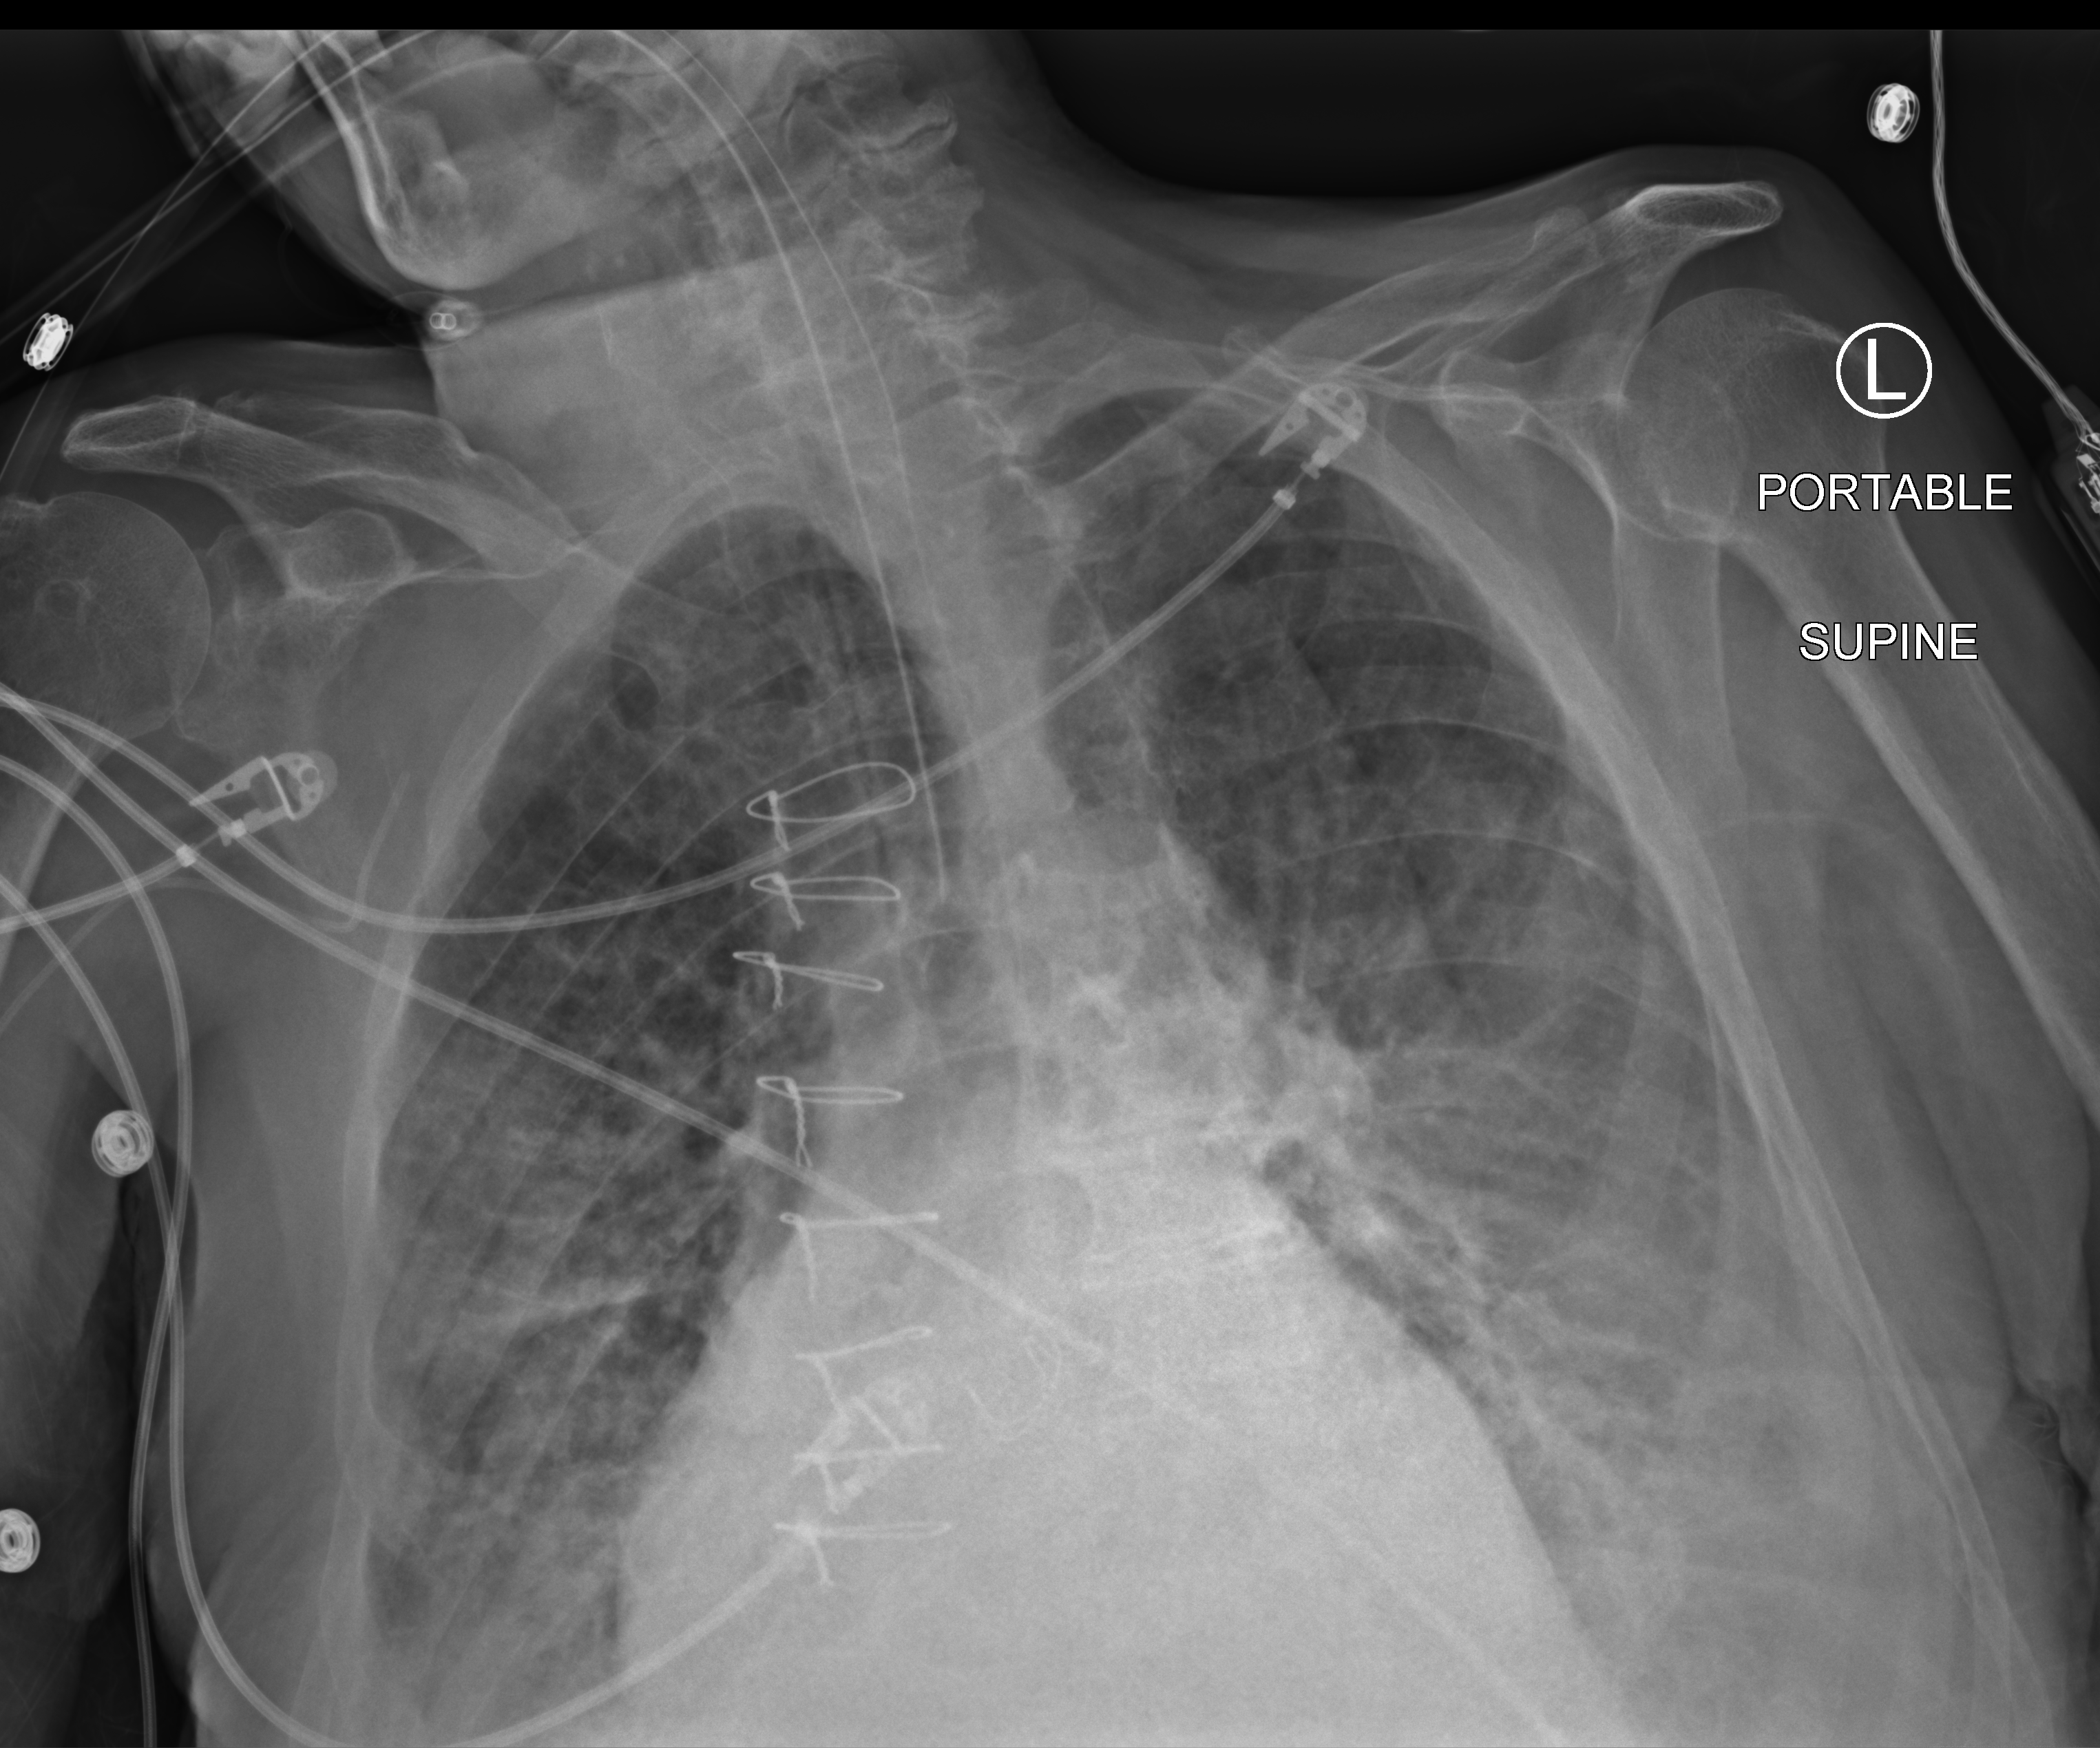
Portable chest radiograph. Male patient hospitalised with COVID-19, age 75–90 years.
From the hospital-stay record, not from the radiograph (when in the stay this image was taken is not recorded): length of hospital stay: 40 days; mechanically ventilated during this hospital stay: yes.